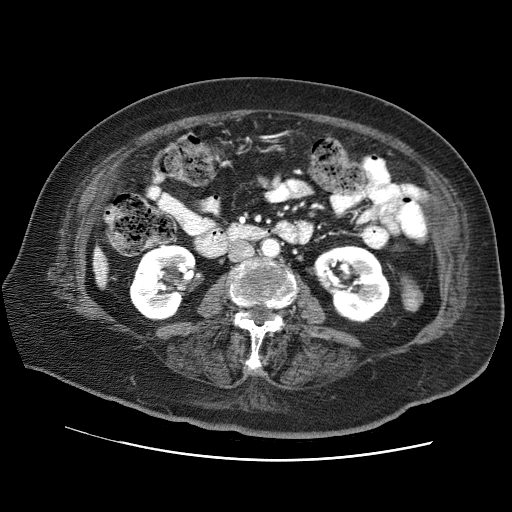
Contrast-enhanced abdominal CT (liver protocol), one axial slice. Position 14 of 73 along the scan axis. 120 kVp. Soft-tissue window (W 400 / L 40 HU). 2.5 mm slice thickness. 512 × 512 image matrix, field of view 380 × 380 mm. Case-level facts recorded for this patient, not image findings: diagnosis: hepatocellular carcinoma (patient treated with transarterial chemoembolisation; whether this scan precedes or follows treatment is not stated here); TNM stage (as recorded): Stage-I; Child-Pugh class: A; tumour differentiation: well differentiated; tumour nodularity: uninodular.
Annotated regions visible in this slice (semi-automatically segmented with operator editing):
- liver parenchyma outside the tumour (the mass and vessels are separate outlines, so this box may not span the whole liver): bounding box <92,247,106,287> (left, top, right, bottom; pixels)